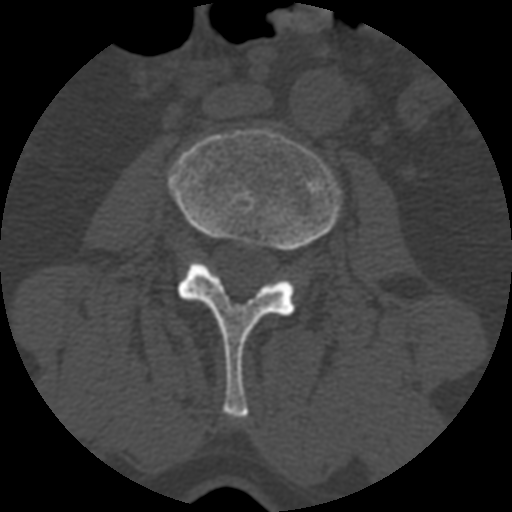
CT including the spine, one axial slice. Slice 303 of 399 in the series (ordered by position). Bone window (W 1800 / L 400 HU). 1.25 mm slice thickness. 512 × 512 image matrix, field of view 160 × 160 mm. Patient age 71 years. Case-level facts recorded for this patient, not image findings: primary cancer: prostate.
Structures marked on this image (semi-automatic segmentation, software-assisted and operator-edited):
- L3 vertebra: box from (x=169, y=128) to (x=343, y=420) px